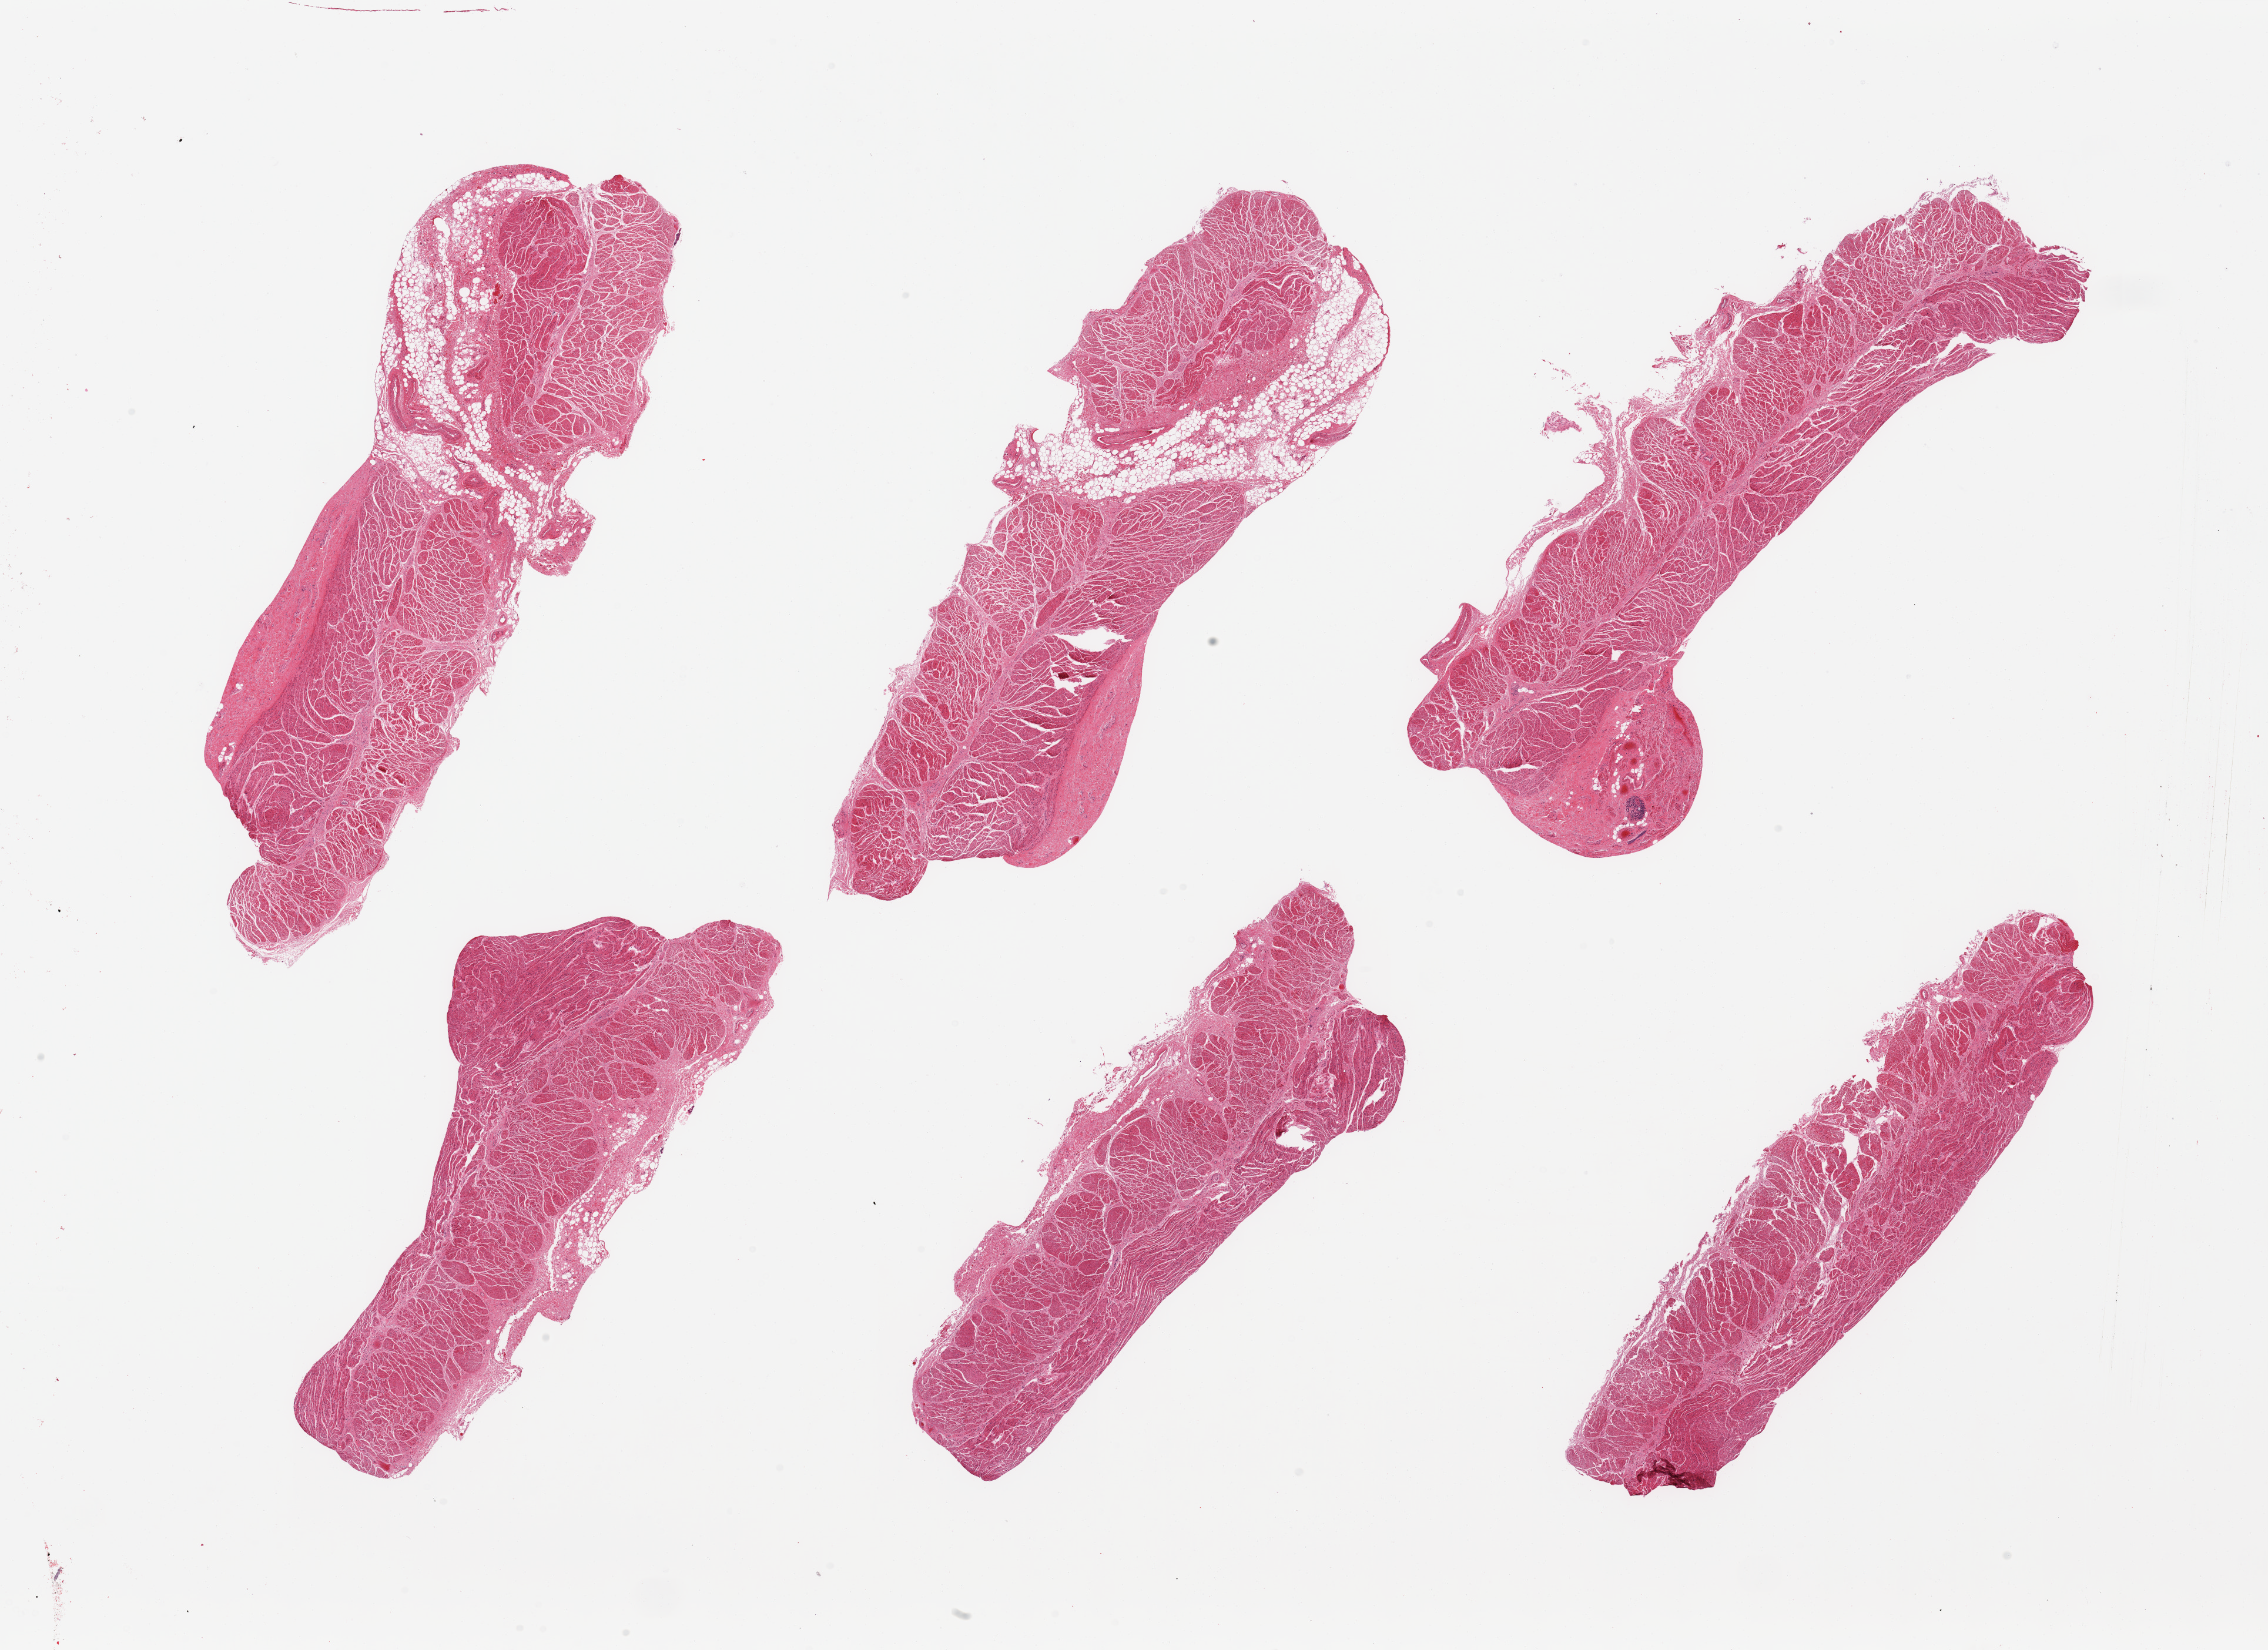
Digitized haematoxylin and eosin-stained section, brightfield — a low-resolution overview of the entire scanned area, about 30.5 x 22.2 mm (slide scanned at 20x), PAXgene-fixed paraffin-embedded (PFPE) section, sampled site (target tissue): gastroesophageal junction, donor tissue sample. Donor: male.
Pathologist's review note for this sample: 6 pieces; minute submucosal gland 0.3 mm; 25% fat in 1 pair.